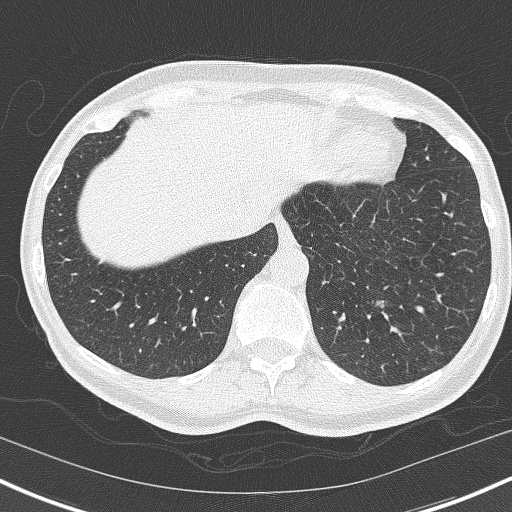
Axial slice from a low-dose chest CT screening exam; second annual screen; lung window (W 1500 / L -600 HU); 2 mm slice thickness; 120 kVp; slice 138 of 171 in the series. Female, age 55 years at enrolment.
Expert-annotated lung lesion, bounding box <354,282,402,329> (left, top, right, bottom; pixels). The exam's reader record, not a measurement of the box and not confirmed to be the same lesion: non-calcified nodule or mass ≥4 mm, right upper lobe, 13 × 6 mm, poorly defined margins, soft tissue attenuation, pre-existing on the prior screen: yes; interval growth: no. Note: the box lies in the patient's left hemithorax on this image, whereas the reader's record names the right lung; they may be different findings. Official screen result: positive, no significant change: stable abnormalities potentially related to lung cancer, unchanged since the prior screening exam. Participant outcome: lung cancer diagnosed 700 days after this screen — adenocarcinoma, NOS, left lower lobe, well differentiated (G1), stage IA (AJCC 6th edition), 11 mm at pathology.